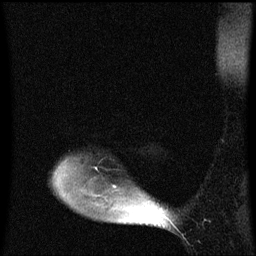
Breast MRI (dynamic contrast-enhanced), one sagittal slice; slice 50 of 60 in the series (ordered by position); dynamic contrast-enhanced series, image 2 of 3 at this slice position (ordered by acquisition); 1.5 T; TE 4.2 ms, TR 8.4 ms; 256 × 256 image matrix, field of view 200 × 200 mm. Patient: female, 49 years. Case-level facts recorded for this patient, not image findings: setting: breast cancer imaged before/during neoadjuvant chemotherapy; receptor status: HR-positive, HER2-negative.
Structures marked on this image (semi-automatic segmentation, software-assisted and operator-edited):
- analysis volume of interest (the breast-tissue region the enhancement analysis was run in; not a lesion): bounding box <54,156,174,221> (left, top, right, bottom; pixels)
- tumour enhancement mask (voxels above the 70 % enhancement threshold inside the analysis volume of interest): <114,186,117,189>